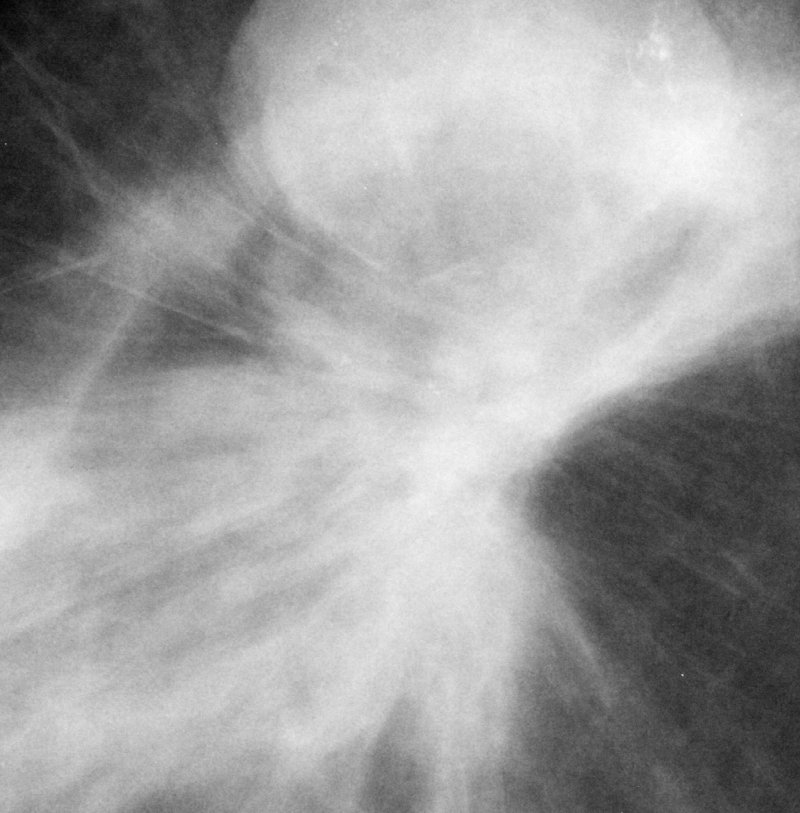
Crop from a digitized film mammogram around one marked abnormality; right breast; CC view; BI-RADS breast density category 2 (scale 1–4).
Marked abnormality: mass, shape irregular, margins spiculated; BI-RADS assessment category 5; pathology (as recorded): malignant.